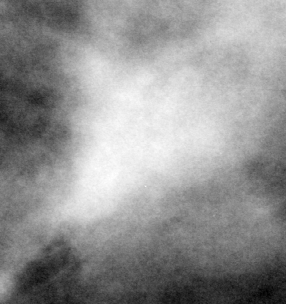
Cropped region of a digitized screen-film mammogram centred on a radiologist-marked abnormality; left breast; CC view; BI-RADS breast density category 2 (scale 1–4).
Finding: mass, shape round, margins obscured; BI-RADS assessment category 4; pathology (as recorded): benign.